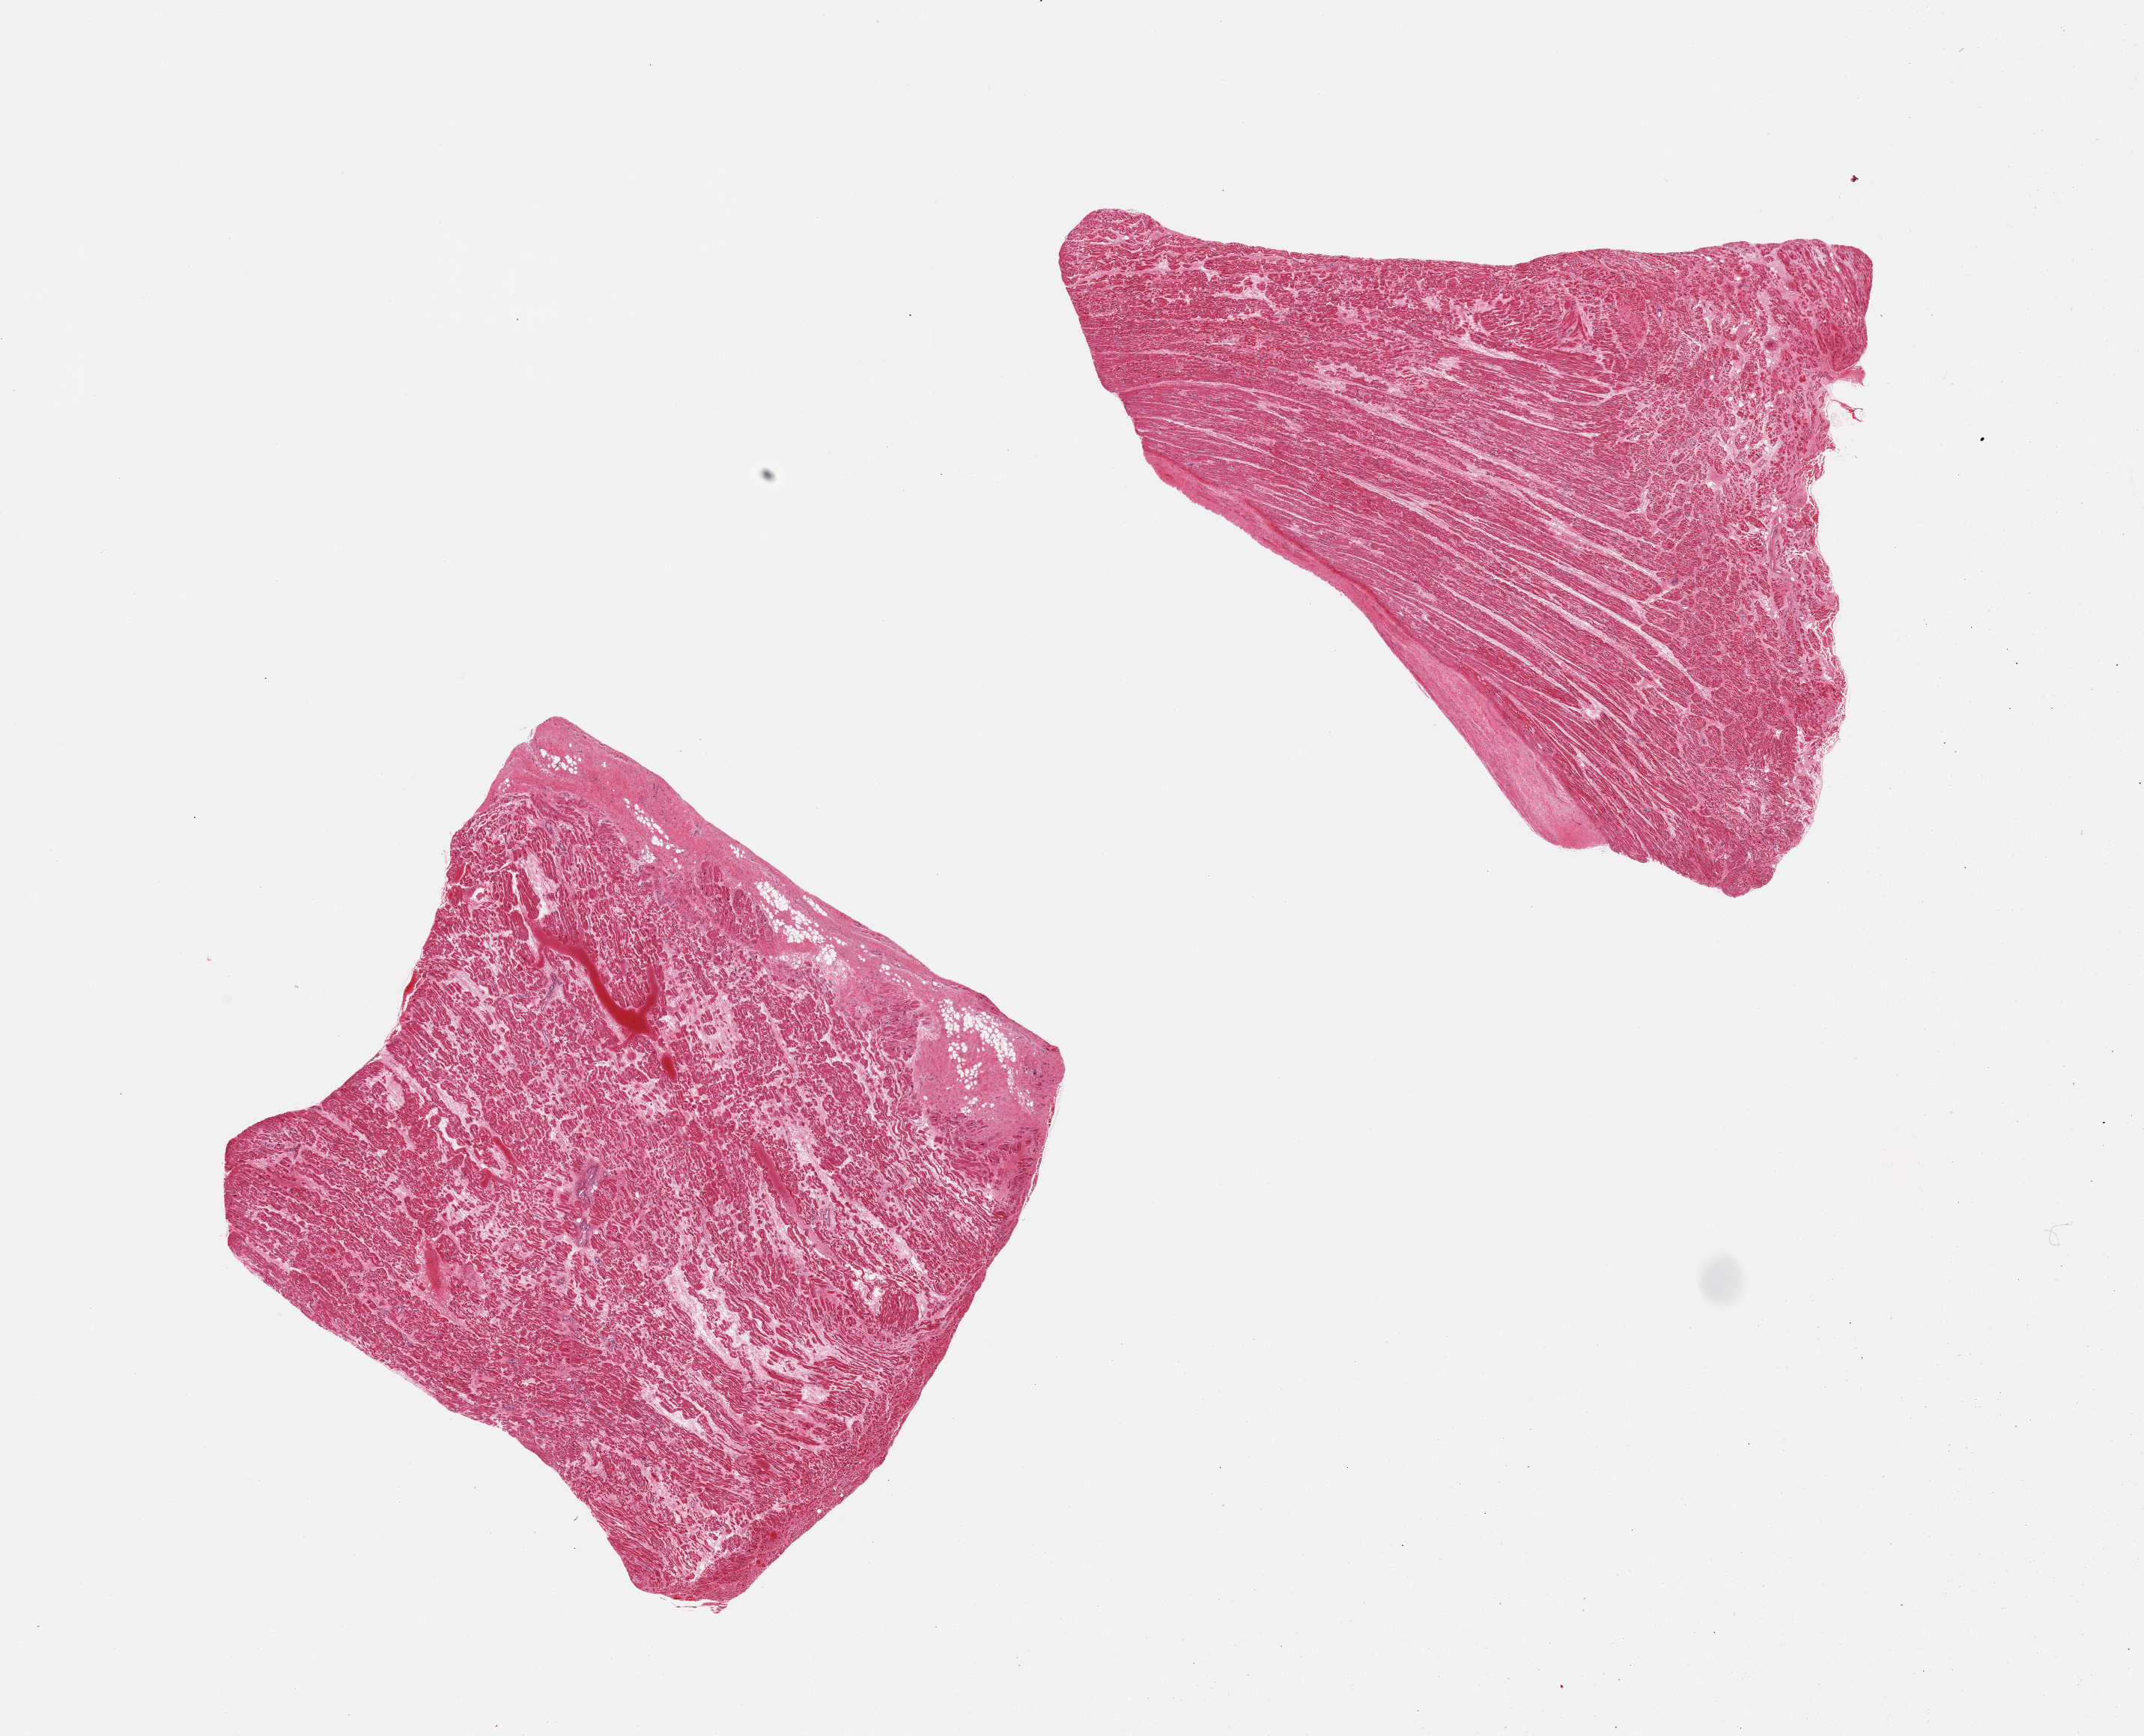
Digitized haematoxylin and eosin-stained section, brightfield — whole scanned area (about 22.6 x 18.3 mm) shown as a low-resolution overview; PAXgene-fixed, paraffin-embedded tissue; sampled site (target tissue): auricular appendage; tissue donor sample. Donor sex: female.
Reviewer comment on this tissue sample: 2 pieces.